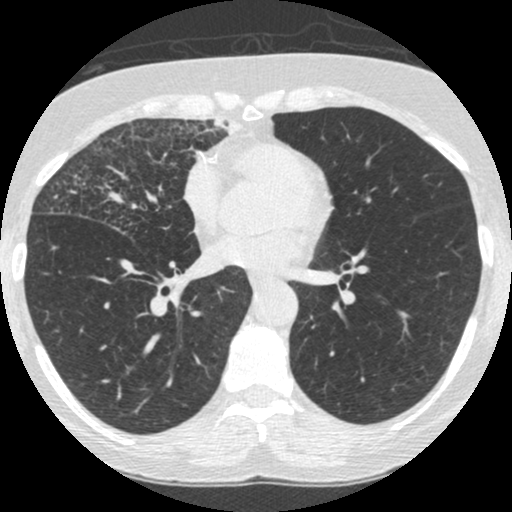
Low-dose screening chest CT, one axial slice; reconstruction kernel STANDARD; lung window (W 1500 / L -600 HU); 1.25 mm slice thickness; 512 × 512 image matrix, field of view 294 × 294 mm.
Outlined on this slice (outlined manually by an expert reader):
- lesion 4 (tumor, upper lobe of right lung): bounding box (x1, y1, x2, y2) in pixels: (190, 116, 242, 154)